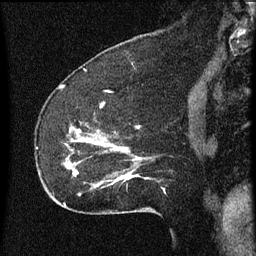
Breast MRI (dynamic contrast-enhanced), one sagittal slice; slice 19 of 60 in the series (ordered by position); dynamic contrast-enhanced series, image 2 of 3 at this slice position (ordered by acquisition); 1.5 T; TE 4.2 ms, TR 8 ms; 2 mm slice thickness; 256 × 256 image matrix, field of view 180 × 180 mm. Female patient, age 52 years.
Annotated regions visible in this slice (semi-automatic segmentation, software-assisted and operator-edited):
- analysis volume of interest (the breast-tissue region the enhancement analysis was run in; not a lesion): bounding box (x1, y1, x2, y2) in pixels: (54, 118, 160, 207)
- tumour enhancement mask (voxels above the 70 % enhancement threshold inside the analysis volume of interest): (65, 126, 139, 181)